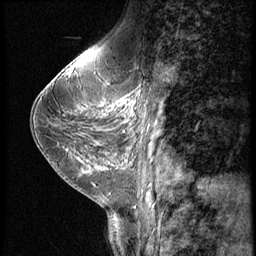
Breast MRI (dynamic contrast-enhanced), one sagittal slice; slice 26 of 56 in the series (ordered by position); dynamic contrast-enhanced series, image 2 of 3 at this slice position (ordered by acquisition); 1.5 T; TE 4.2 ms, TR 9 ms; 2.5 mm slice thickness; 256 × 256 image matrix, field of view 180 × 180 mm. Patient: female, 38 years. From the clinical record (not read from this slice): setting: breast cancer imaged before/during neoadjuvant chemotherapy; receptor status: triple-negative.
Annotated regions visible in this slice (semi-automatic segmentation, software-assisted and operator-edited):
- analysis volume of interest (the breast-tissue region the enhancement analysis was run in; not a lesion): bounding box <107,95,148,149> (left, top, right, bottom; pixels)
- tumour enhancement mask (voxels above the 140 % enhancement threshold inside the analysis volume of interest): <113,98,135,113>